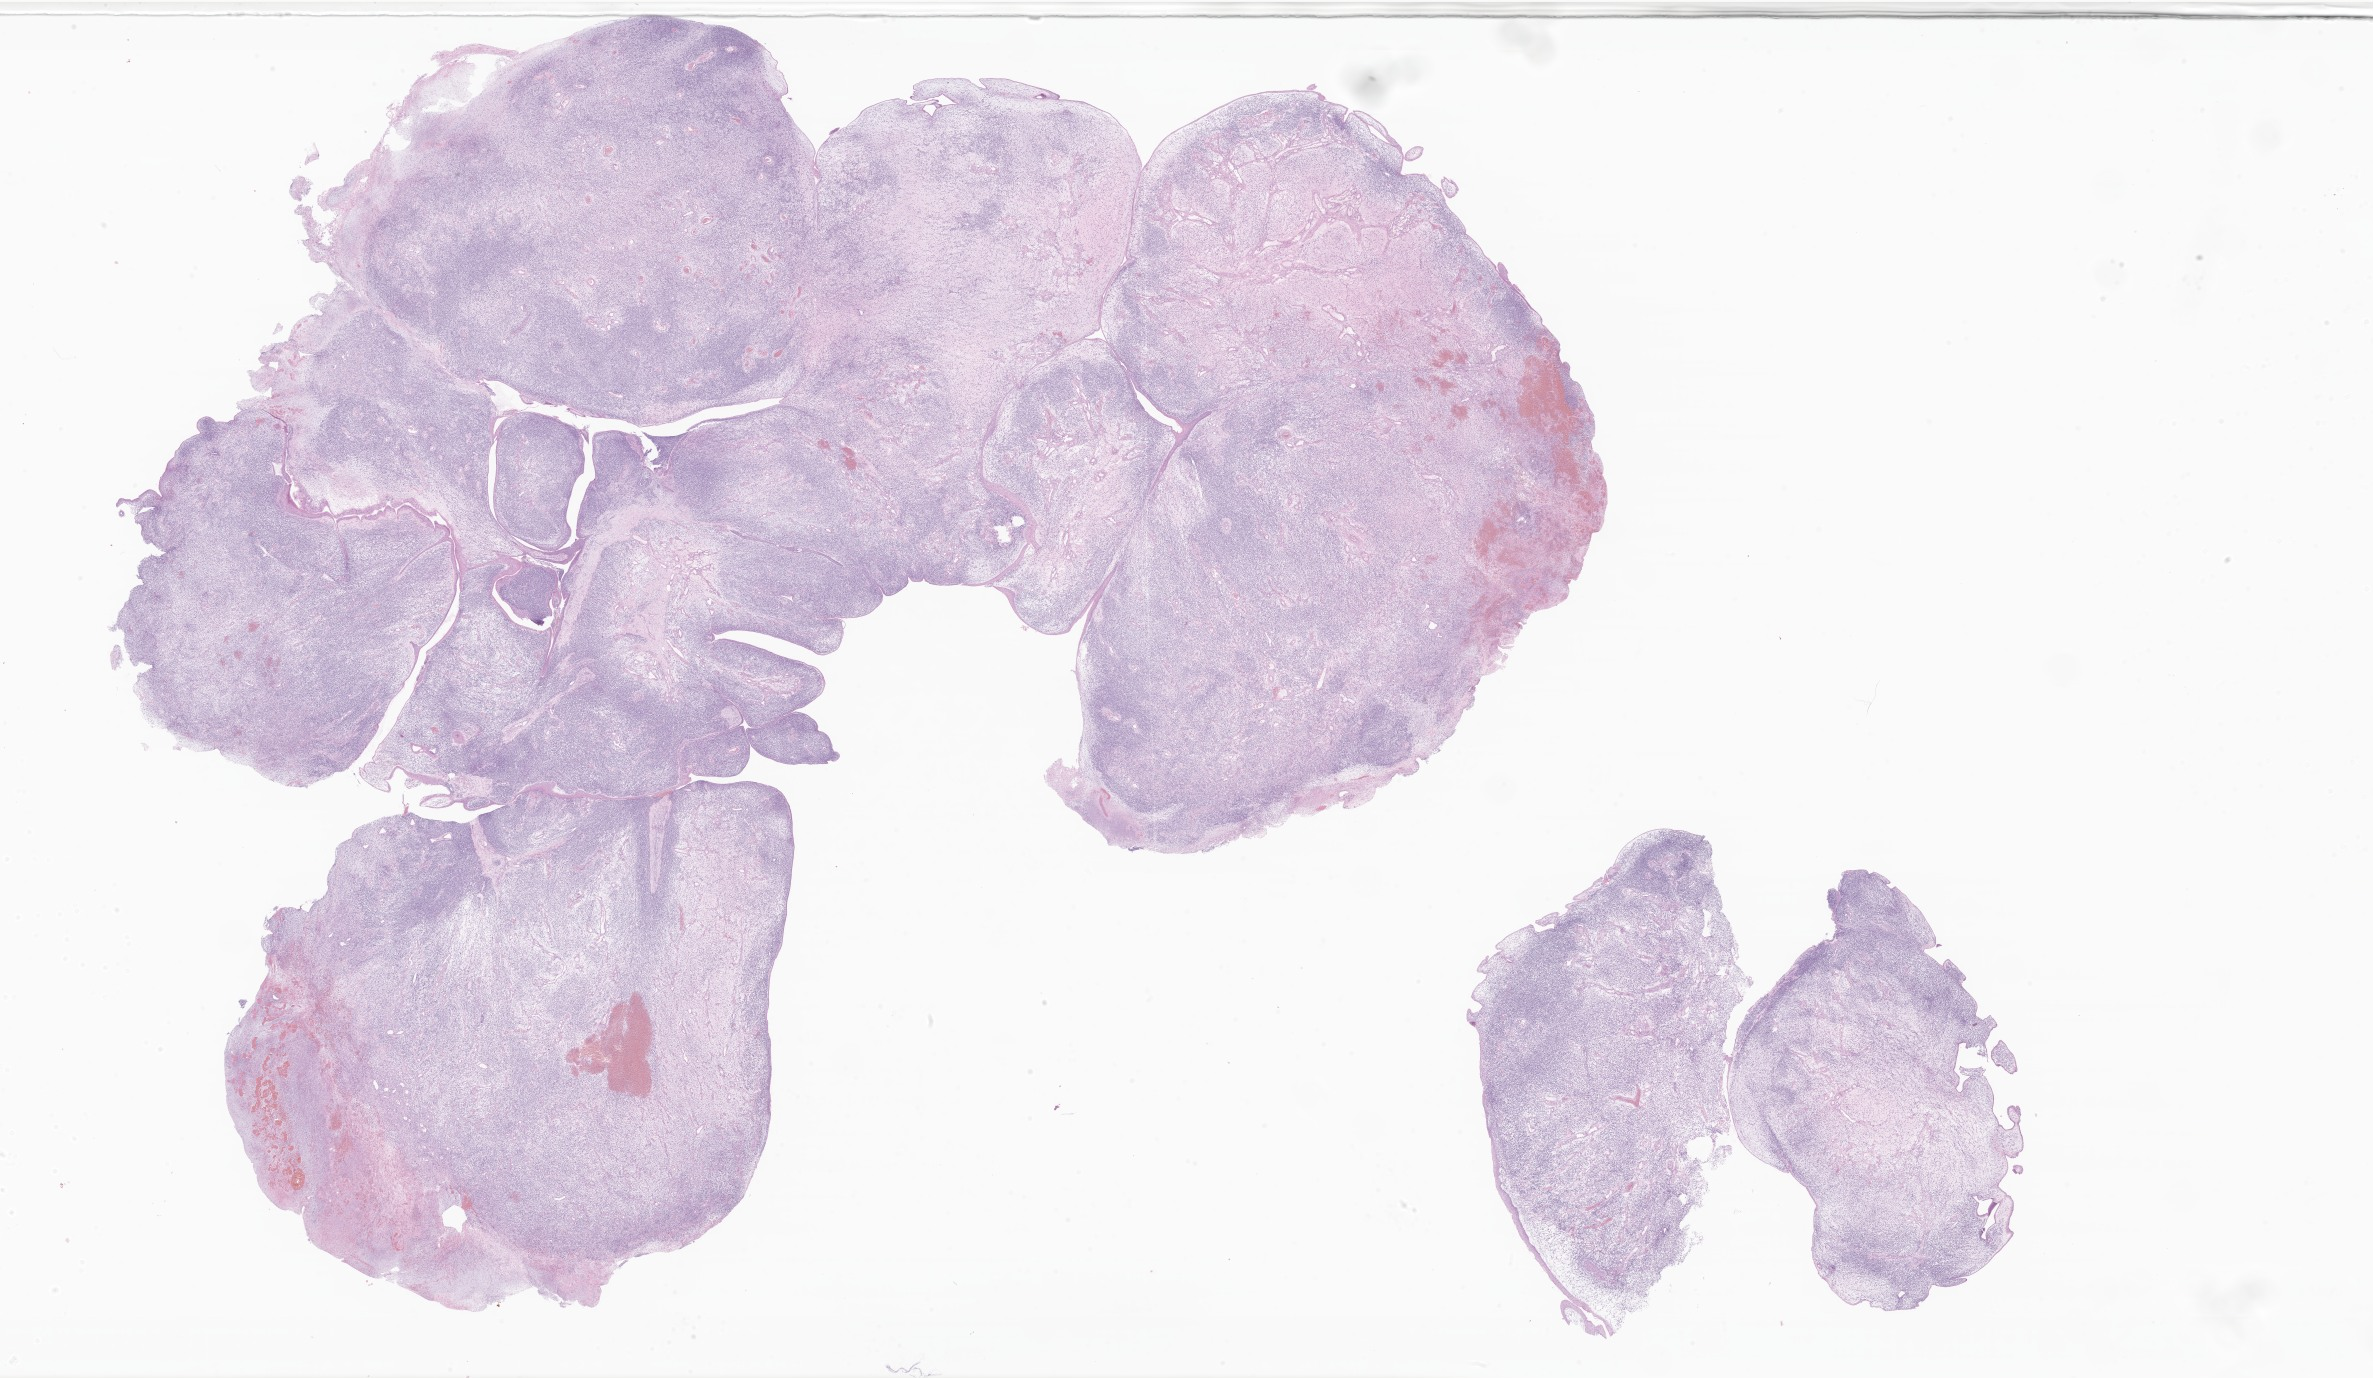
Whole-slide image, H&E stain of tumor tissue from the nasopharynx — a low-resolution overview of the entire scanned area, about 40.0 x 23.2 mm; formalin-fixed, paraffin-embedded (FFPE) tissue. Female patient, age 56 months.
Diagnosis: Embryonal rhabdomyosarcoma, NOS.